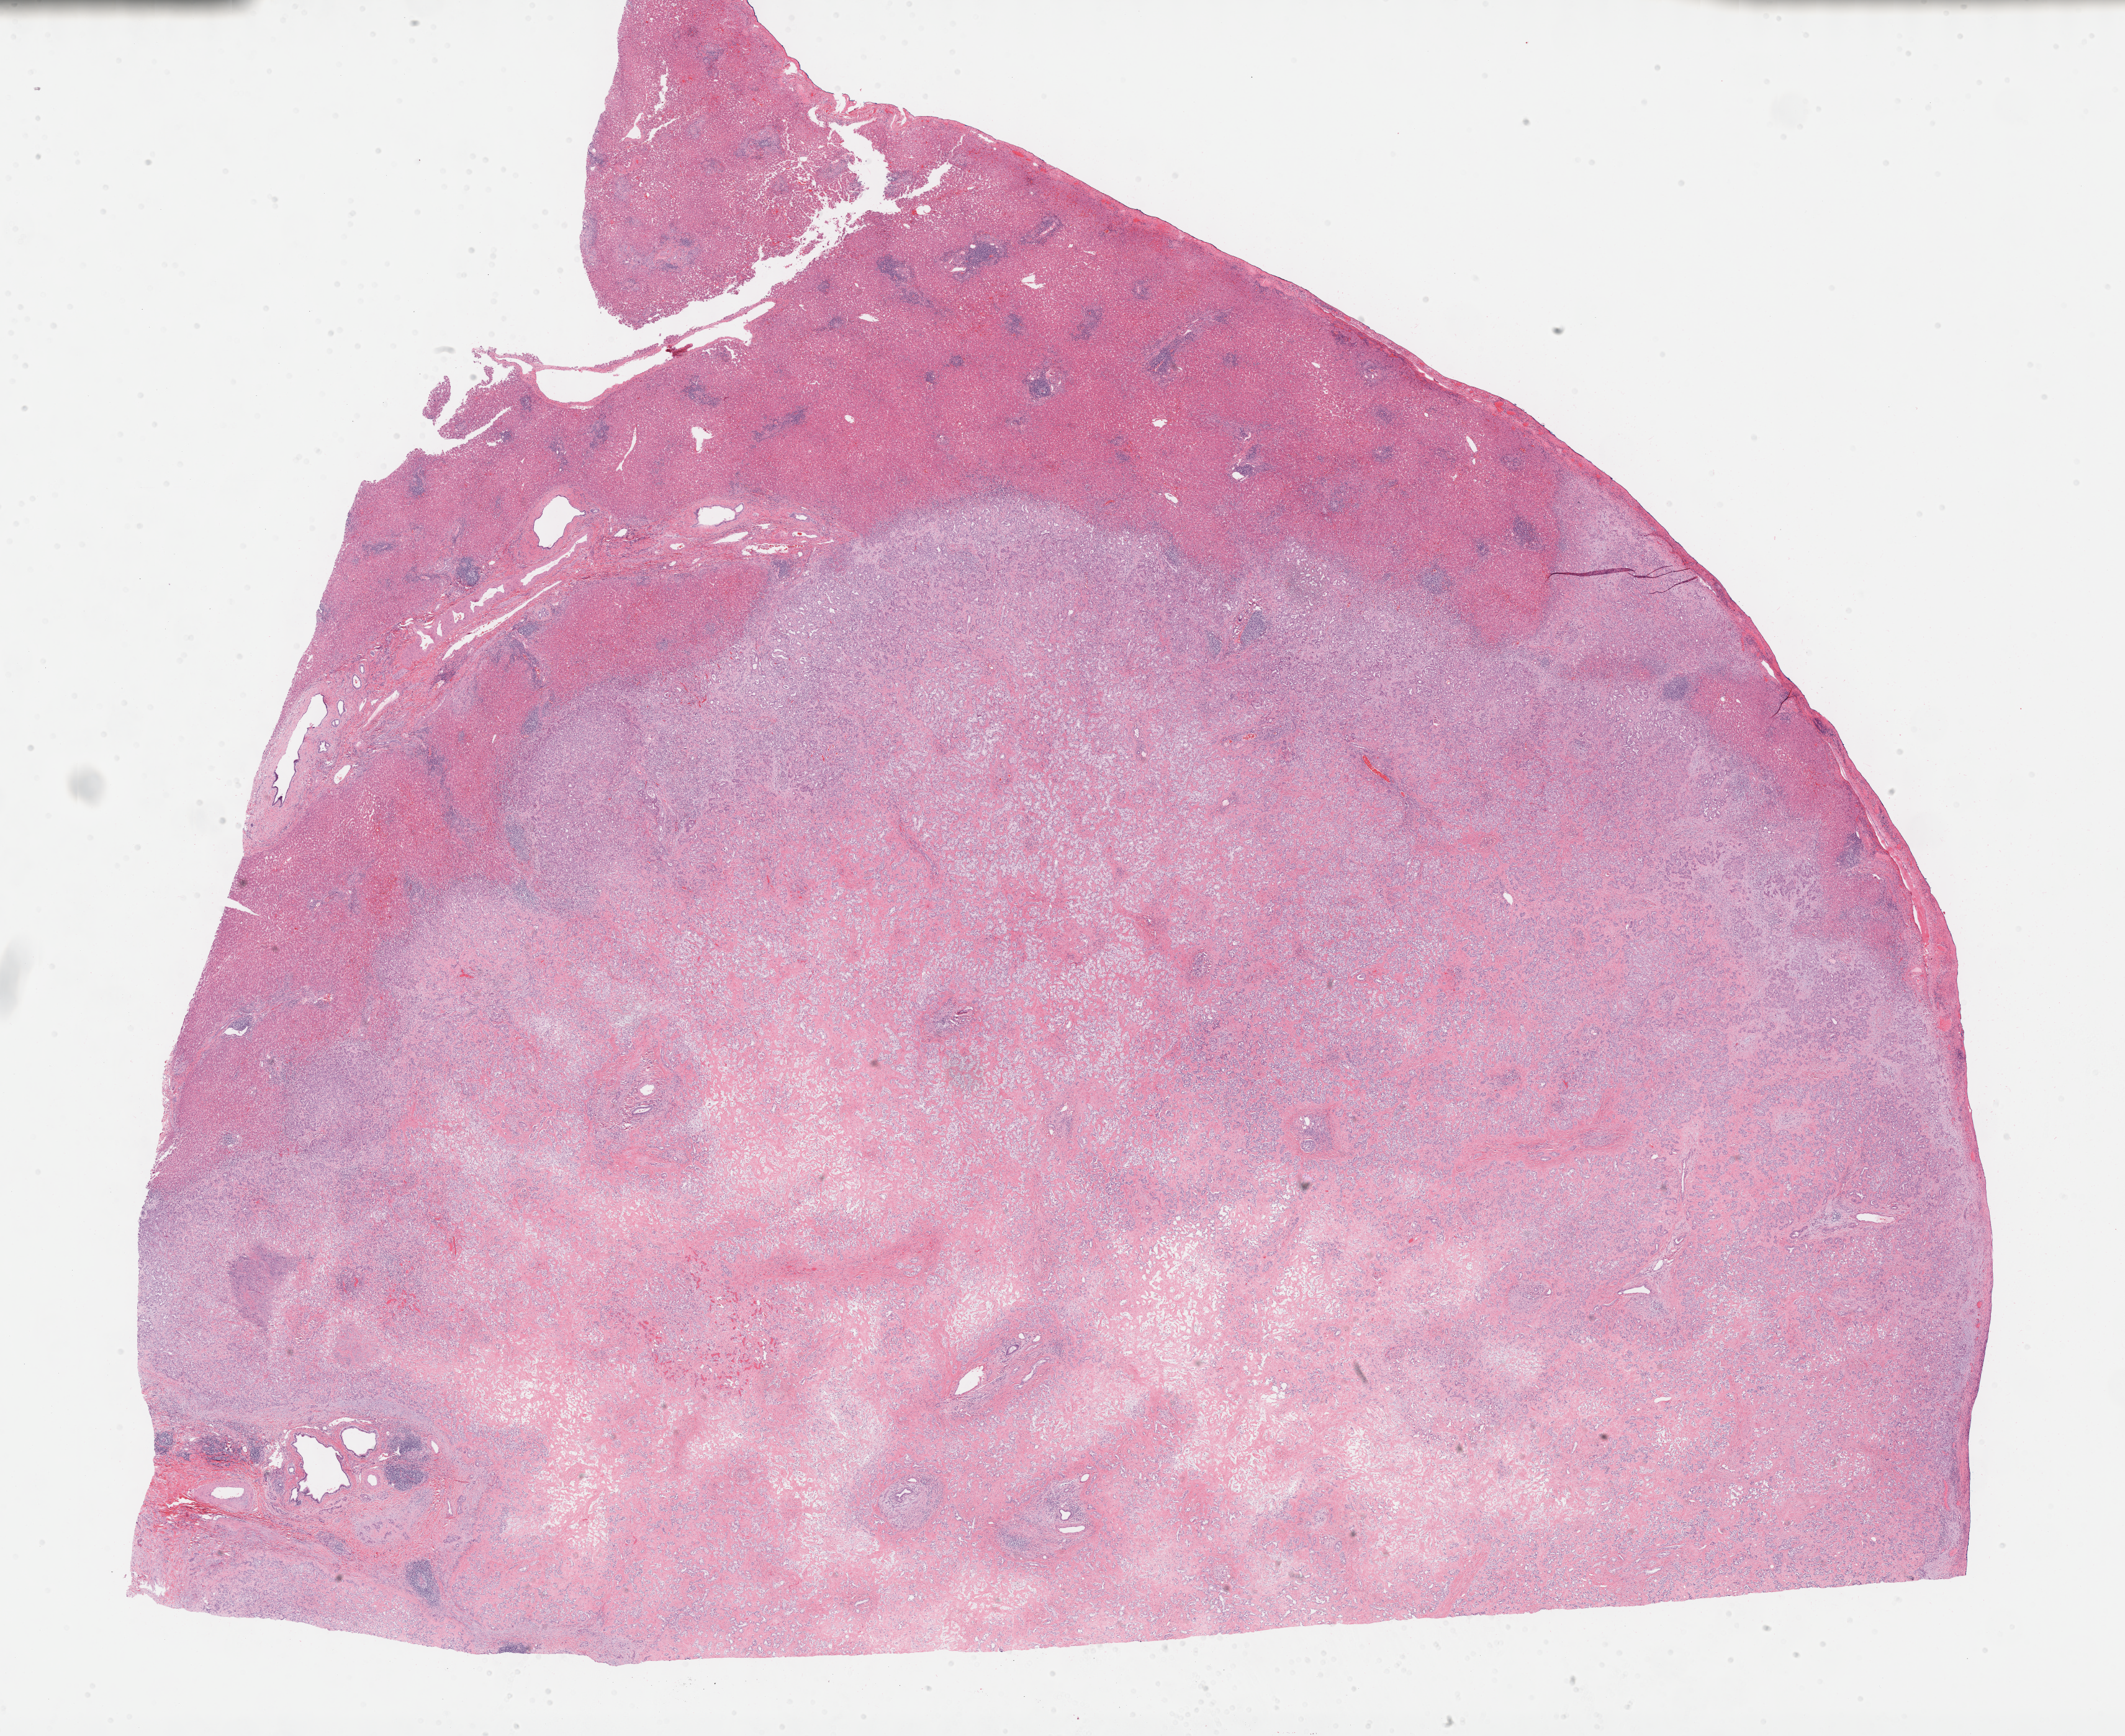
Whole-slide histology image, Hematoxylin and eosin (H&E) stained, a low-resolution overview of the entire scanned area, about 27.7 x 22.6 mm (slide scanned at 40x). Formalin-fixed paraffin-embedded (FFPE) diagnostic section. Primary tumour sample from the bile duct. Female patient; age at initial diagnosis 46 years. Histologic grade: G2 (moderately differentiated).
Pathologic diagnosis: Cholangiocarcinoma (intrahepatic bile duct). AJCC pathologic stage: I (7th edition).